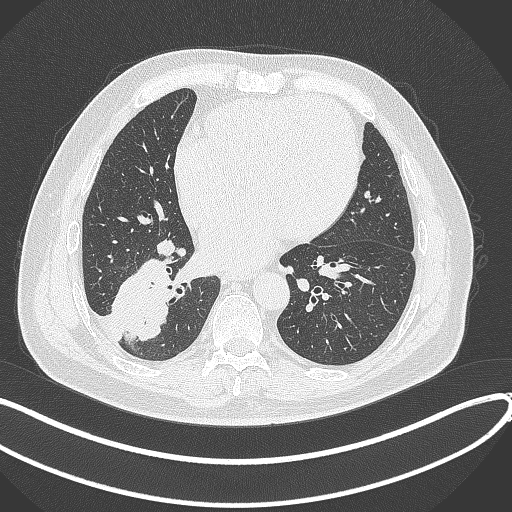
Chest CT, one axial slice. Slice 139 of 360 in the series (ordered by position). Lung window (W 1500 / L -600 HU). 1 mm slice thickness. 512 × 512 image matrix. Male patient, age 59 years.
Structures marked on this image (bounding box drawn by a radiologist):
- lung tumour (recorded histology: adenocarcinoma): bounding box <107,257,180,342> (left, top, right, bottom; pixels)